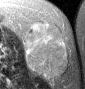
MRI of an extremity soft-tissue mass, one axial slice. Position 17 of 46 along the scan axis. T2-weighted fat-saturated. MR volume resampled by the dataset authors to the PET/CT grid (not the native acquisition matrix). 85 × 89 image matrix, field of view 83 × 87 mm. Female patient. From the clinical record (not read from this slice): histological type: leiomyosarcoma; grade: intermediate; site of the primary tumour: parascapusular.
Outlined on this slice (expert contour drawn on MRI and transferred to this co-registered scan by the dataset authors):
- gross tumour volume including surrounding oedema: bounding box [x1, y1, x2, y2] px = [25, 23, 69, 77]
- gross tumour volume (mass): [25, 23, 69, 77]